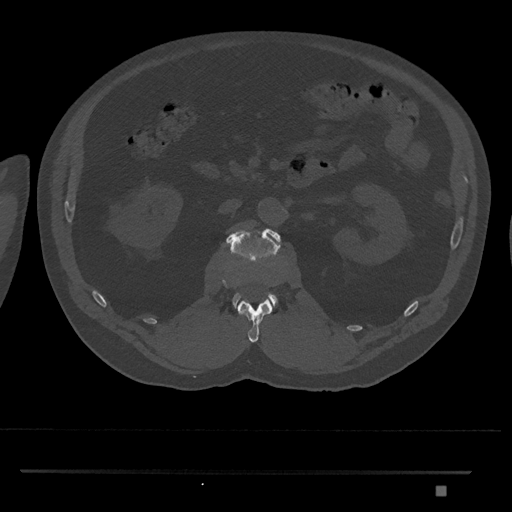
CT including the spine, one axial slice. Position 792 of 1134 along the scan axis. 120 kVp. Bone window (W 1800 / L 400 HU). 512 × 512 image matrix, field of view 429 × 429 mm. Male patient, age 65 years. Case-level facts recorded for this patient, not image findings: primary cancer: prostate.
Outlined on this slice (semi-automatically segmented with operator editing):
- L1 vertebra: bounding box [x1, y1, x2, y2] px = [238, 299, 272, 343]
- L2 vertebra: [226, 228, 281, 309]